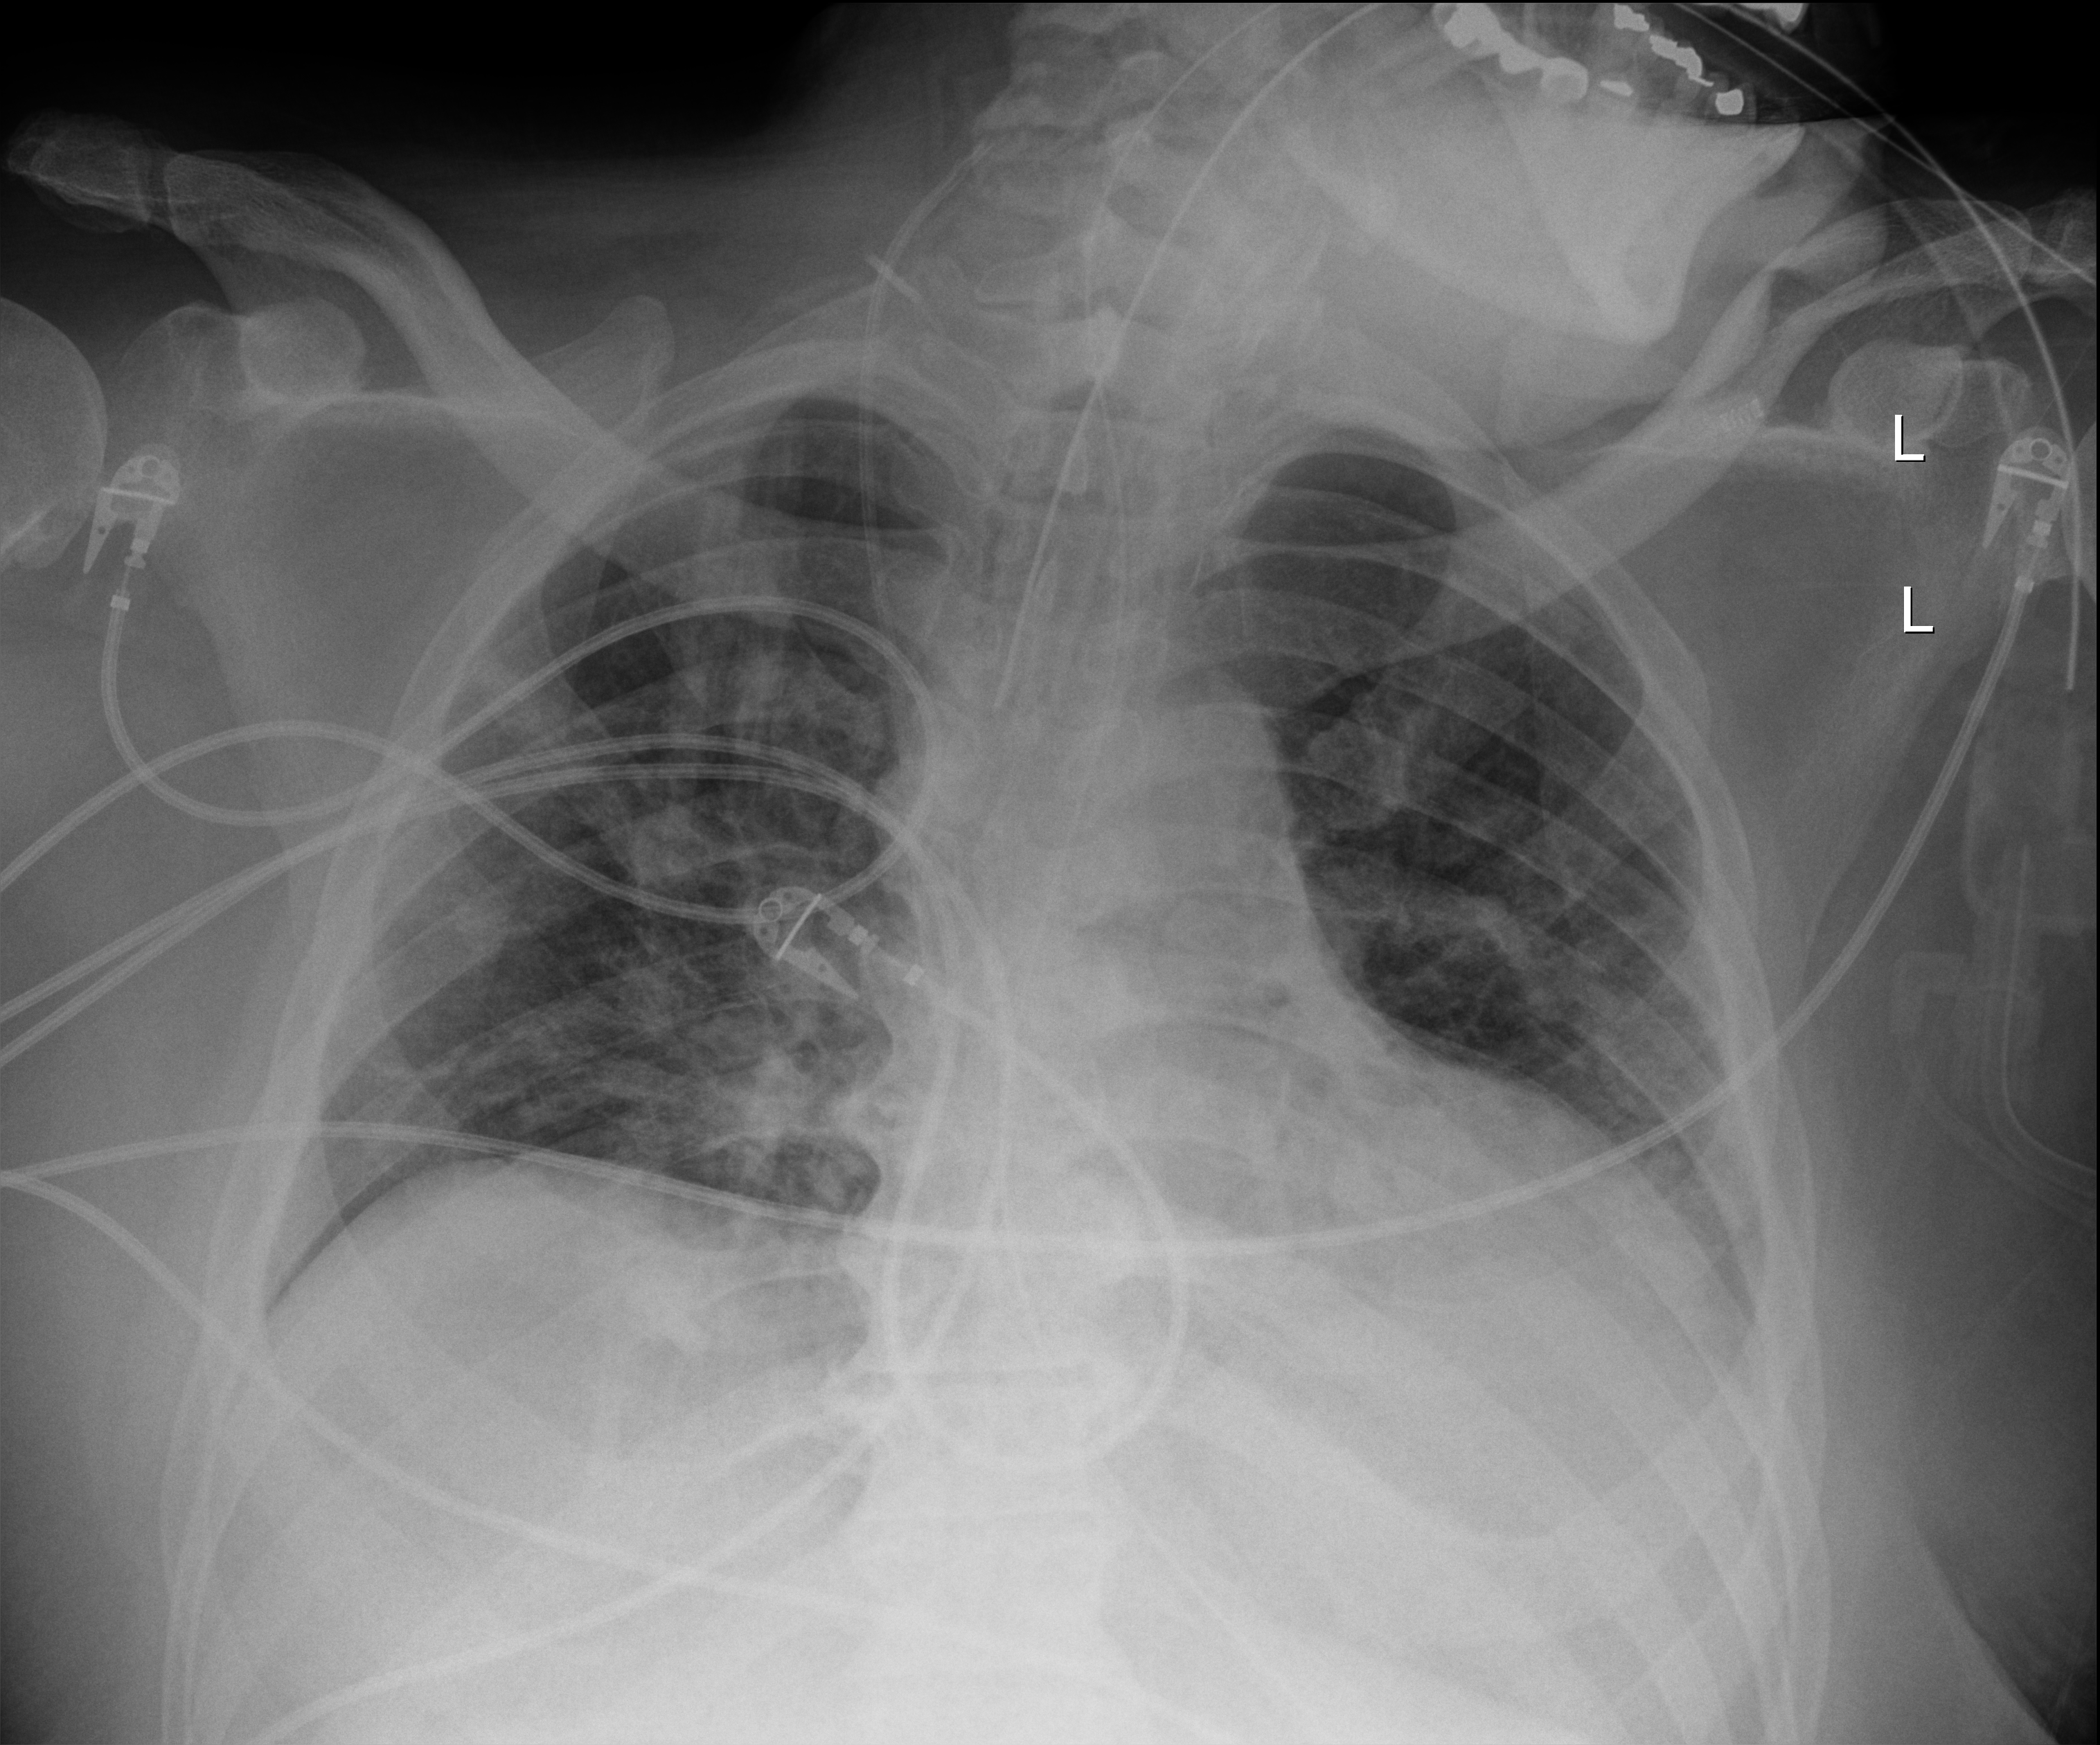
Chest X-ray (portable); anteroposterior (AP) projection. Patient hospitalised with COVID-19; male, aged 18–59 years.
Admission-level facts for this patient (not findings on this image; timing relative to this image not recorded): admitted to intensive care during this hospital stay: yes; length of hospital stay: 41 days.